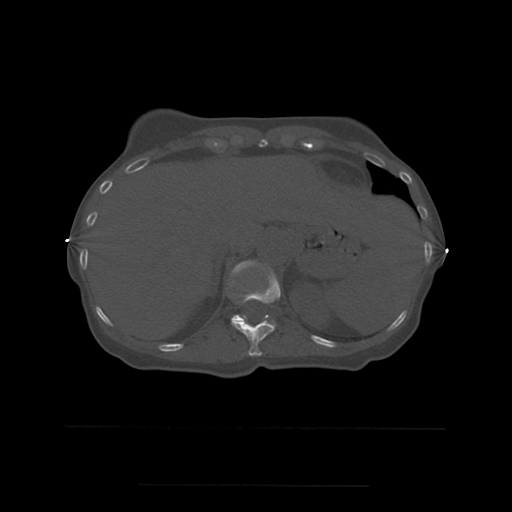
CT including the spine, one axial slice; slice 273 of 544 in the series (ordered by position); bone window (W 1800 / L 400 HU); 1.25 mm slice thickness; 512 × 512 image matrix, field of view 350 × 350 mm. Patient age 58 years. Case-level facts recorded for this patient, not image findings: primary cancer: lung.
Structures marked on this image (semi-automatically segmented with operator editing):
- T11 vertebra: bounding box (x1, y1, x2, y2) in pixels: (231, 273, 281, 357)
- T12 vertebra: (231, 261, 279, 322)